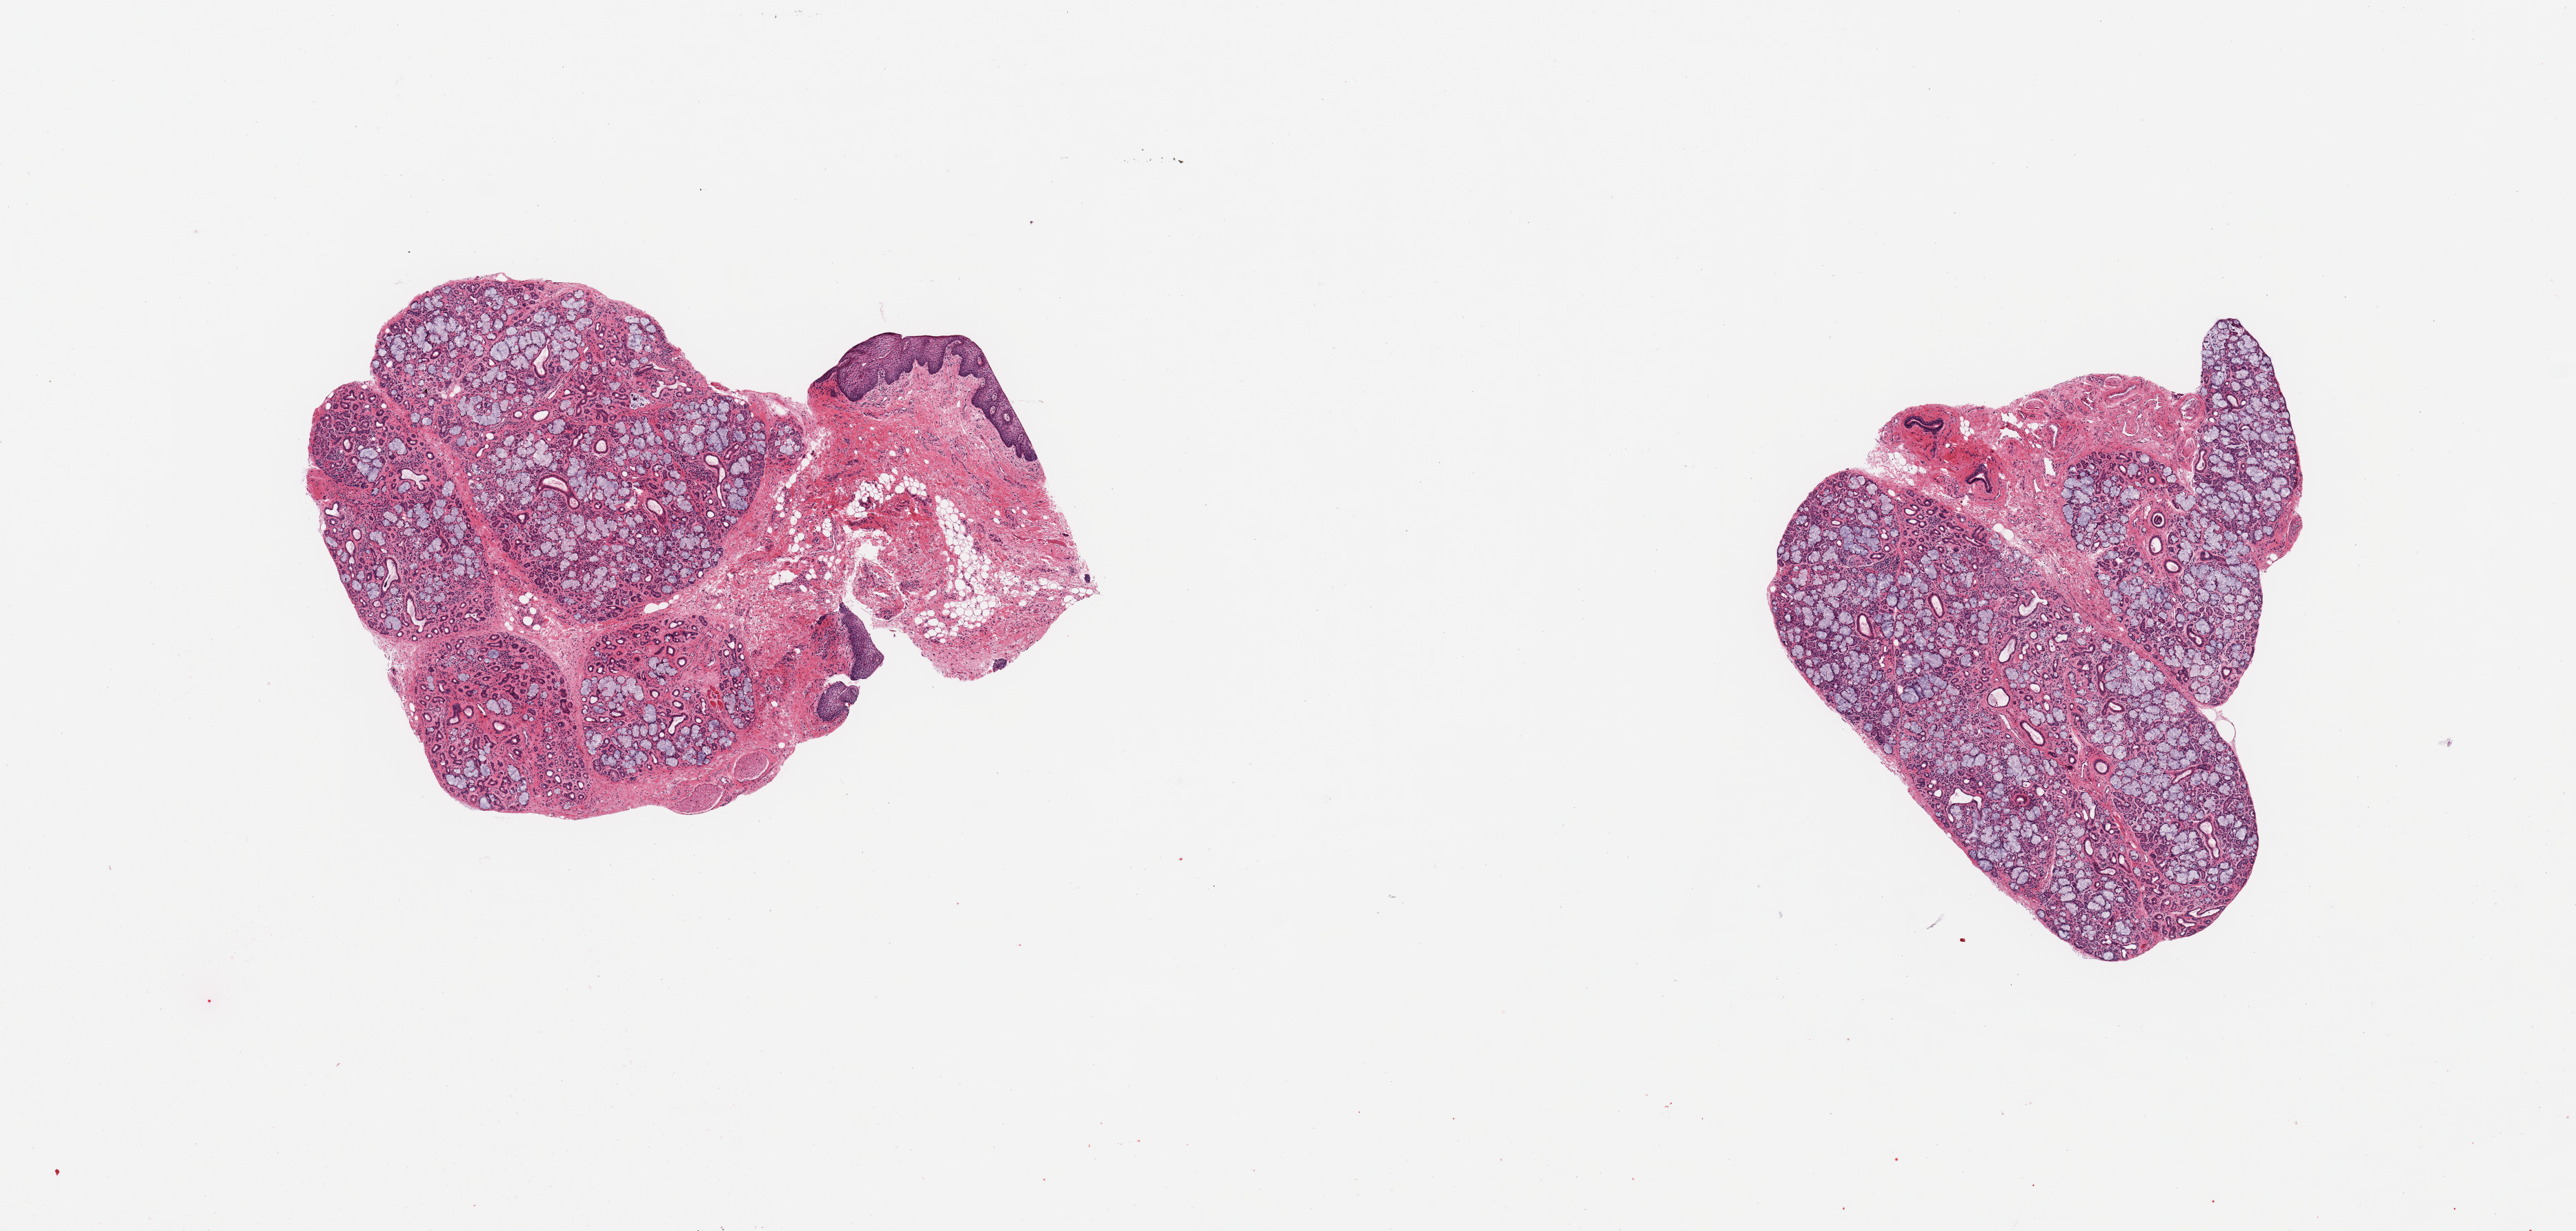
Haematoxylin and eosin whole-slide image, whole scanned area (about 14.8 x 7.1 mm, slide scanned at 20x) shown as a low-resolution overview; PAXgene-fixed paraffin-embedded (PFPE) section; target tissue: minor salivary gland; tissue donor sample.
Review note (as recorded): 2 pieces, ~80% glandular elements, rest is connective elements/squamous mucosa.